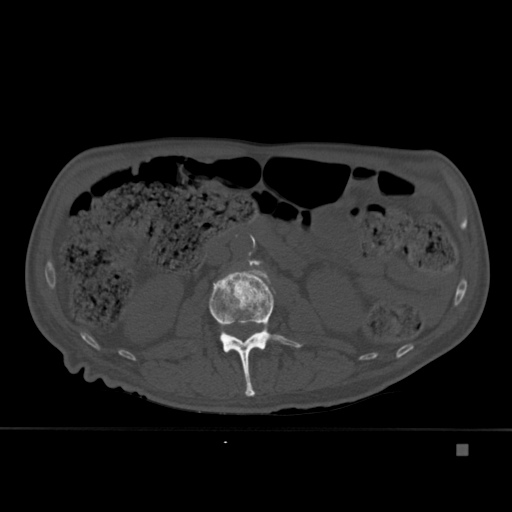
CT including the spine, one axial slice. Position 160 of 451 along the scan axis. Bone window (W 1800 / L 400 HU). 1.5 mm slice thickness. 512 × 512 image matrix. Male patient, age 75 years. From the clinical record (not read from this slice): primary cancer: prostate.
Outlined on this slice (semi-automatically segmented with operator editing):
- L2 vertebra: bounding box (x1, y1, x2, y2) in pixels: (209, 265, 303, 397)
- L3 vertebra: (248, 259, 263, 267)